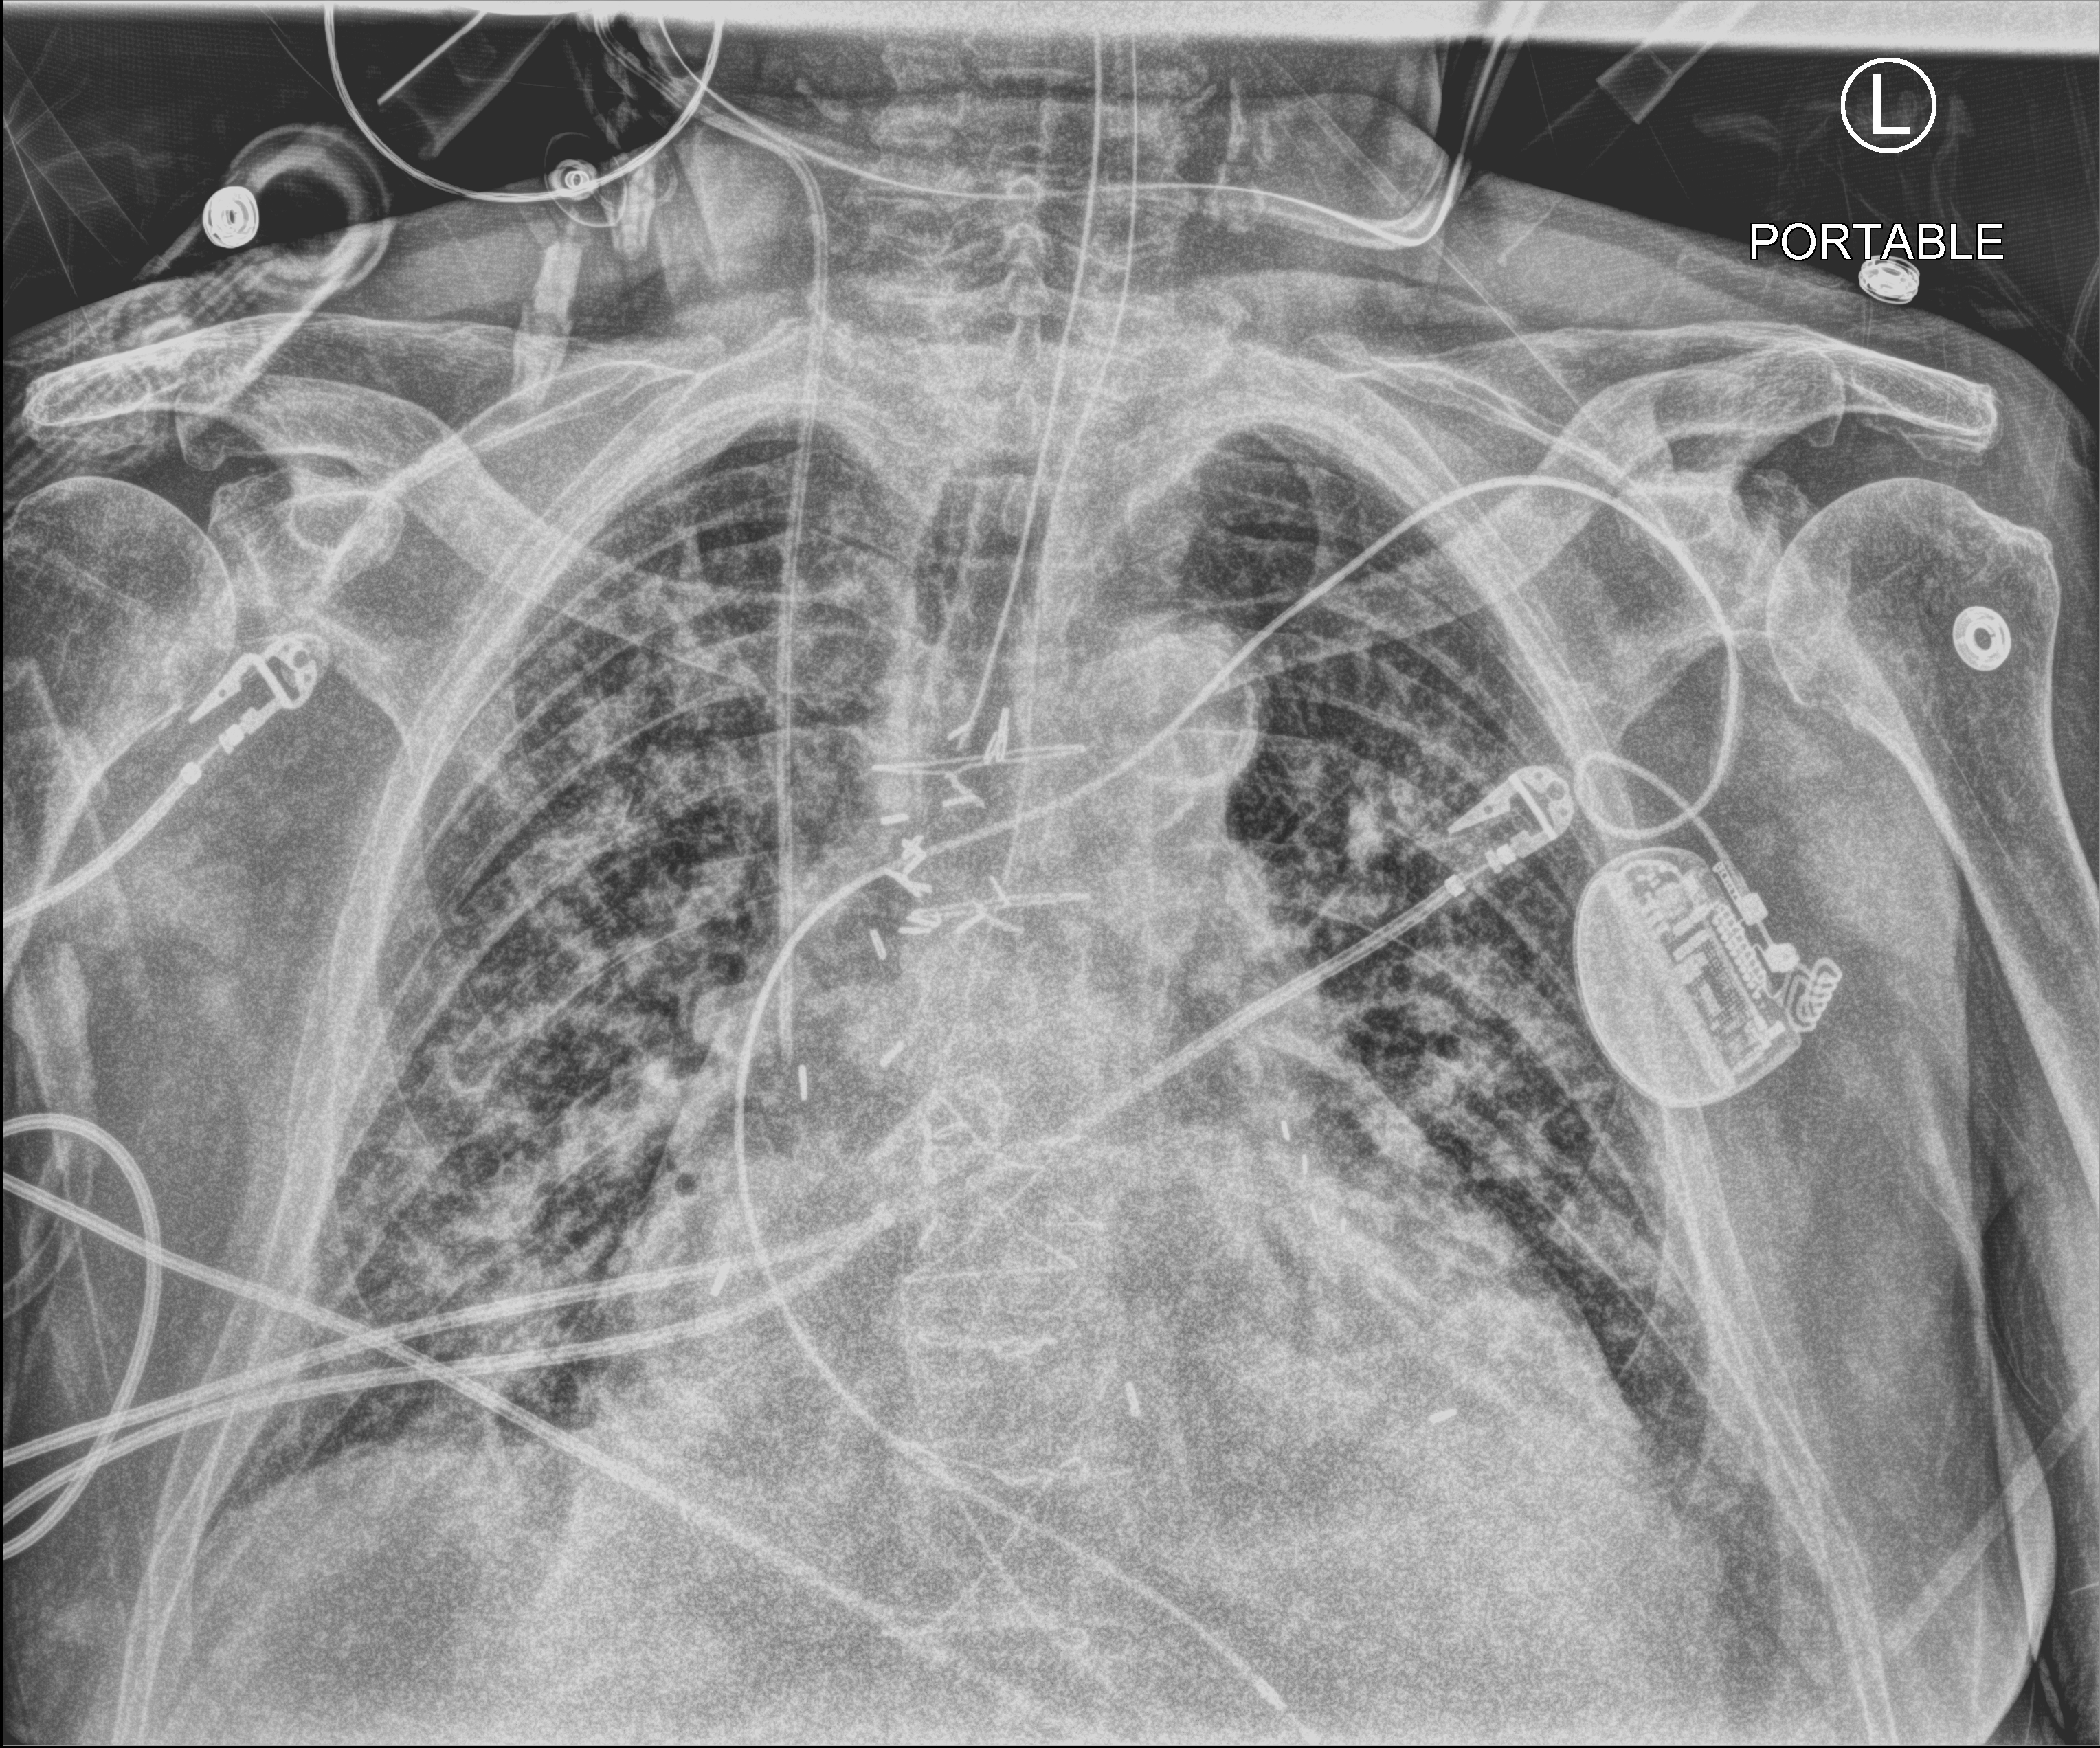
Bedside chest radiograph (computed radiography); anteroposterior (AP) projection. Male patient hospitalised with COVID-19, age 75–90 years.
Hospital-stay facts (about this admission, not read from this image; timing relative to this image not recorded): mechanically ventilated during this hospital stay: yes.